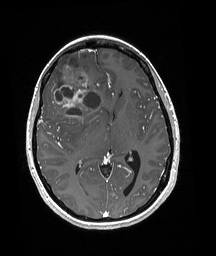
Brain MRI from a brain-tumour surgery series, one axial slice. Slice 99 of 192 in the series (ordered by position). T1-weighted post-contrast. 1 mm slice thickness. 216 × 256 image matrix. Case-level facts recorded for this patient, not image findings: histopathology: Oligodendroglioma; WHO grade: 3; IDH mutation: yes.
Annotated regions visible in this slice (manually delineated by an expert):
- tumour: bounding box (x1, y1, x2, y2) in pixels: (47, 54, 101, 118)